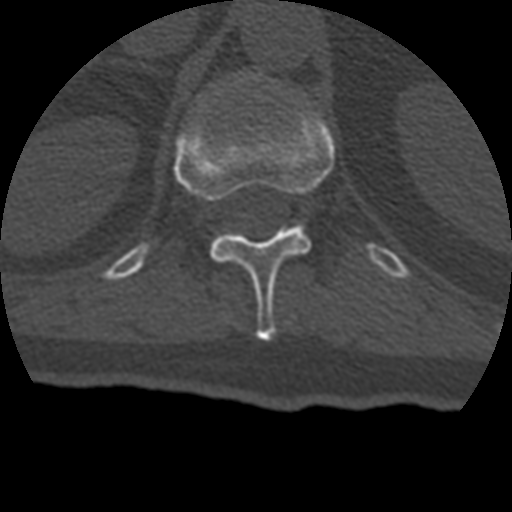
CT including the spine, one axial slice. Position 166 of 399 along the scan axis. Reconstruction kernel STANDARD. Bone window (W 1800 / L 400 HU). 1.25 mm slice thickness. 512 × 512 image matrix, field of view 160 × 160 mm. Patient age 69 years. Case-level facts recorded for this patient, not image findings: primary cancer: prostate.
Annotated regions visible in this slice (semi-automatically segmented with operator editing):
- T12 vertebra: box from (x=174, y=109) to (x=335, y=341) px